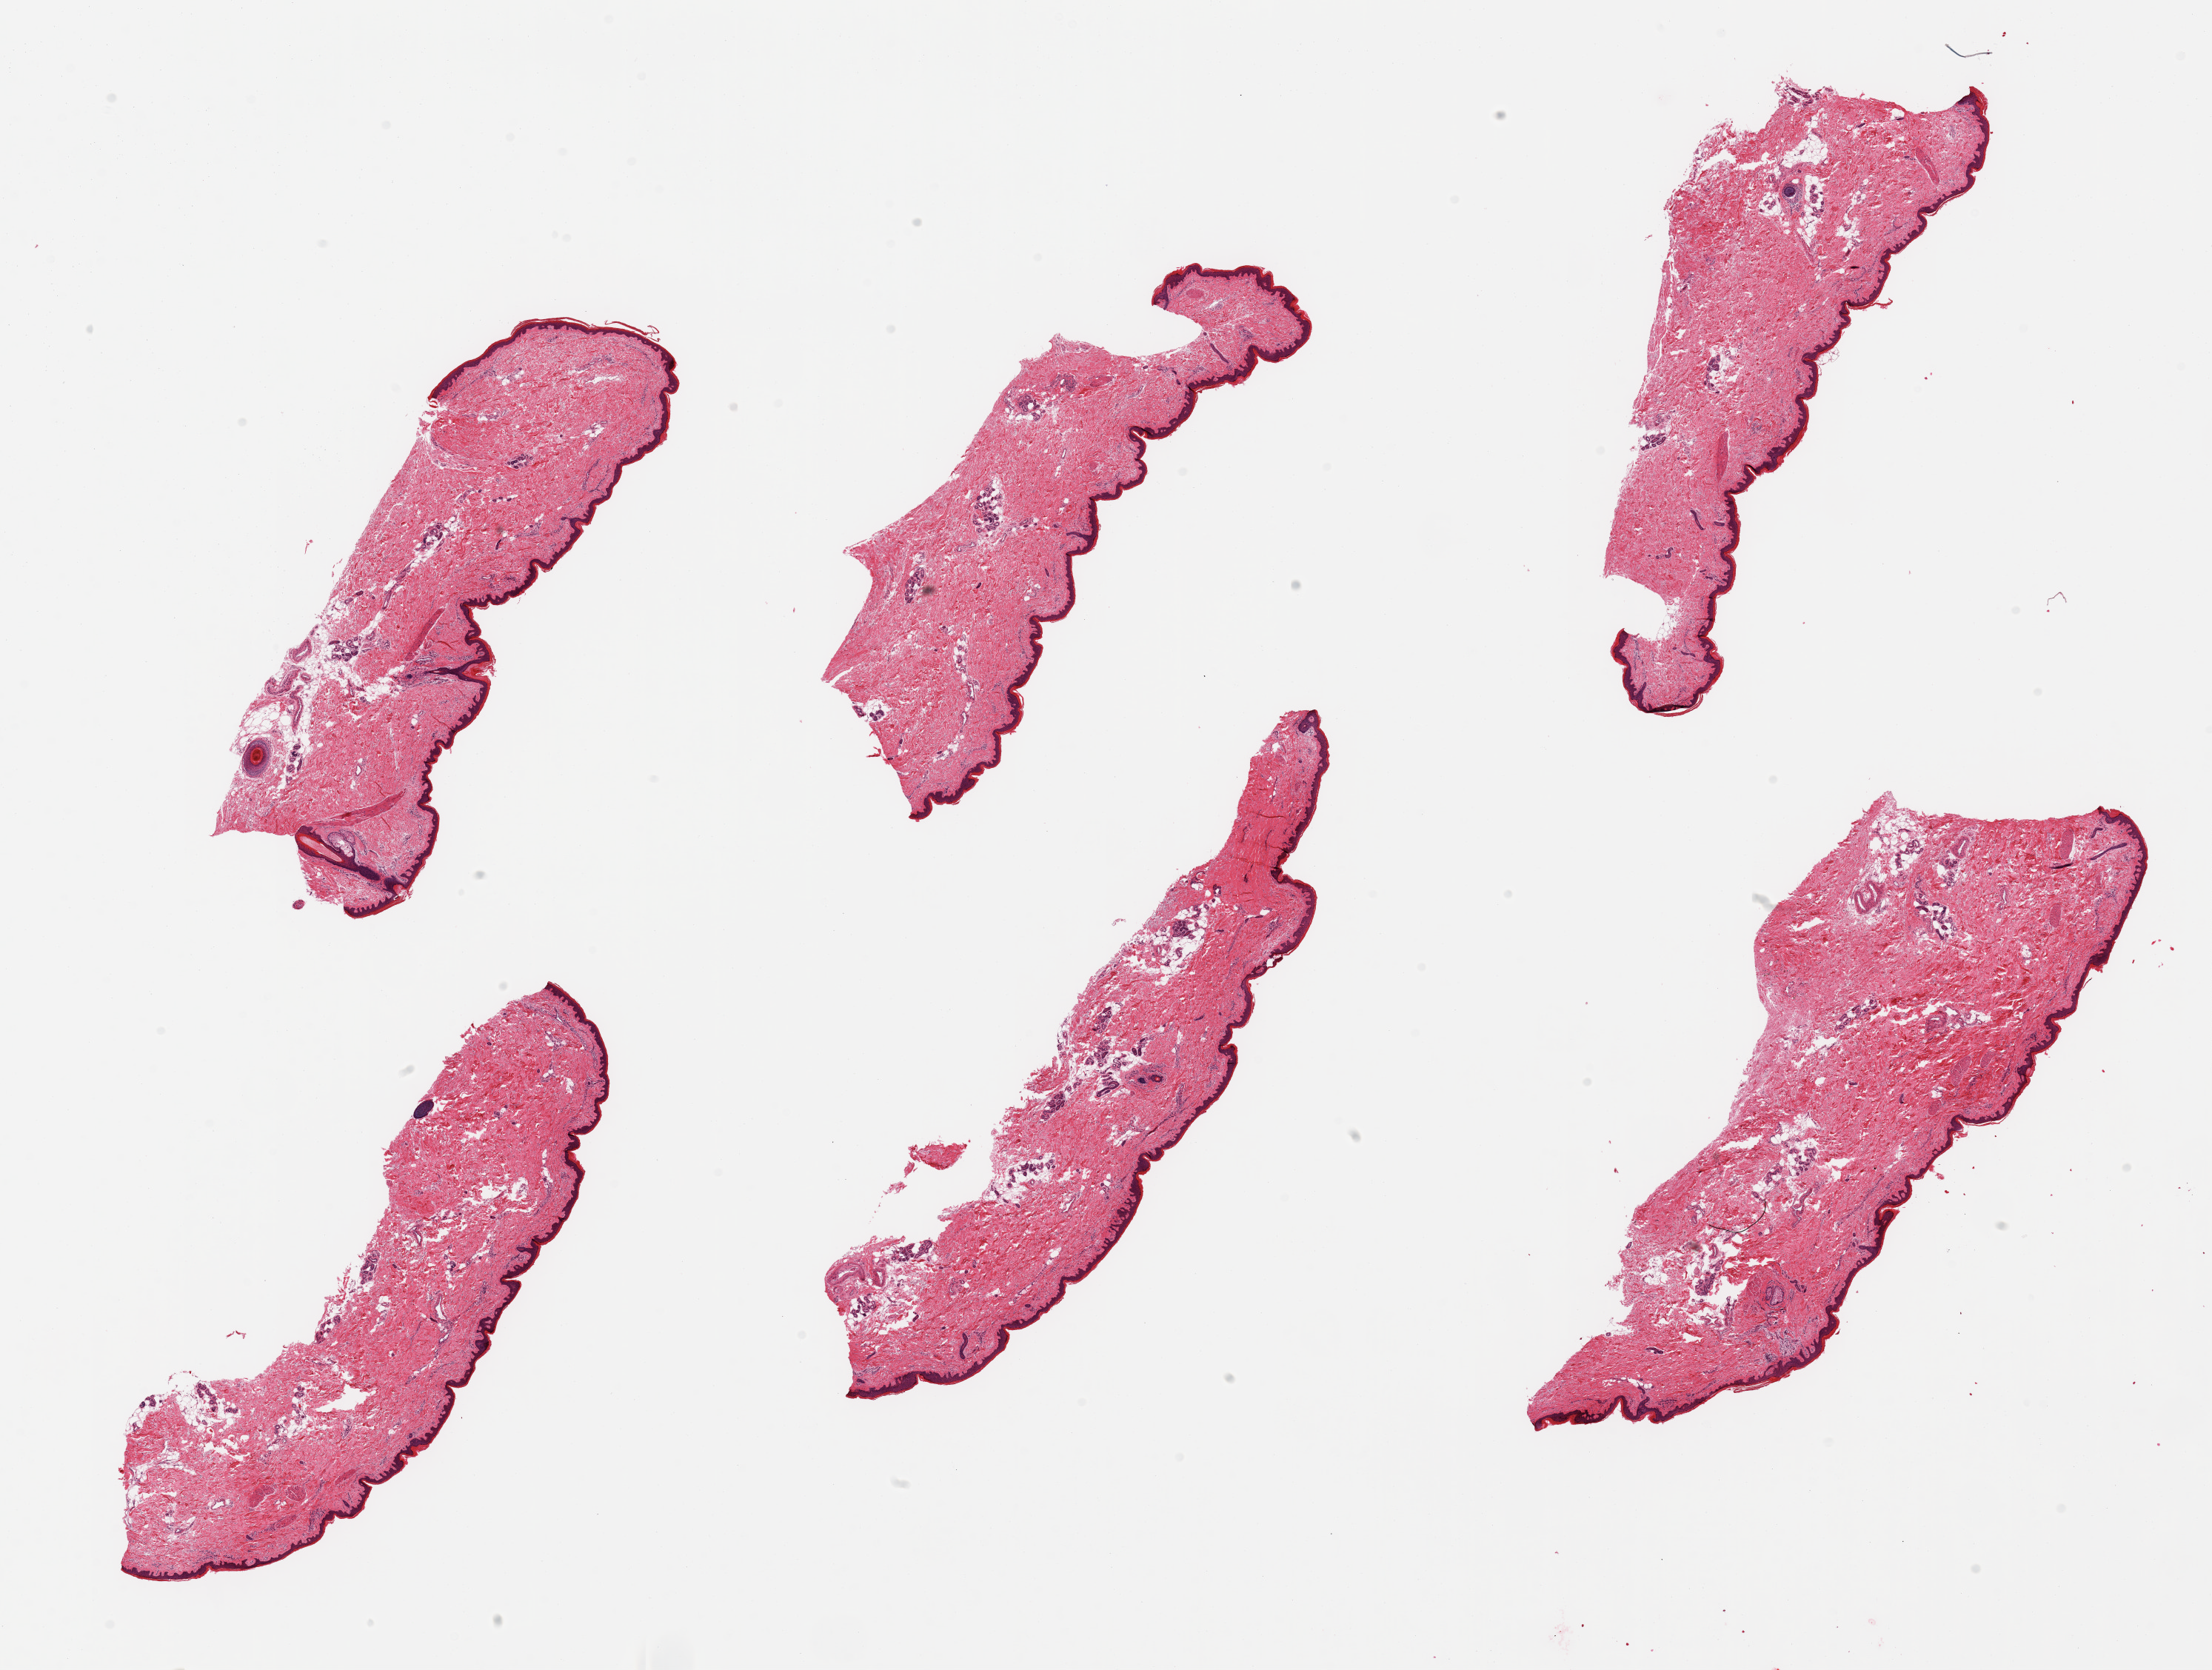
Digitized hematoxylin and eosin (H&E)-stained section, a low-resolution overview of the entire scanned area, about 23.6 x 17.8 mm (slide scanned at 20x), PAXgene-fixed paraffin-embedded (PFPE) section, sampled site (target tissue): skin of lower leg, tissue donor sample. Donor: male.
Review note (as recorded): 6 pieces, minimal adherent dermal fat; squamous epthelium is ~30-40 microns.